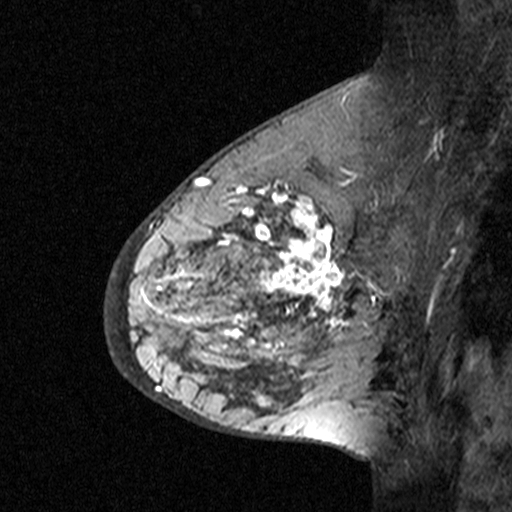
Breast MRI (dynamic contrast-enhanced), one sagittal slice. Slice 24 of 44 in the series (ordered by position). Dynamic contrast-enhanced study with each time point stored as its own series, time point 3 of 4 at this slice position (ordered by acquisition time). 1.5 T. TE 4.5 ms, TR 11 ms. 3 mm slice thickness. 512 × 512 image matrix, field of view 200 × 200 mm. Patient: female, 65 years. From the clinical record (not read from this slice): setting: breast cancer imaged before/during neoadjuvant chemotherapy; receptor status: HER2-positive.
Outlined on this slice (semi-automatic segmentation, software-assisted and operator-edited):
- analysis volume of interest (the breast-tissue region the enhancement analysis was run in; not a lesion): bounding box (x1, y1, x2, y2) in pixels: (182, 190, 353, 361)
- tumour enhancement mask (voxels above the 90 % enhancement threshold inside the analysis volume of interest): (216, 190, 345, 351)